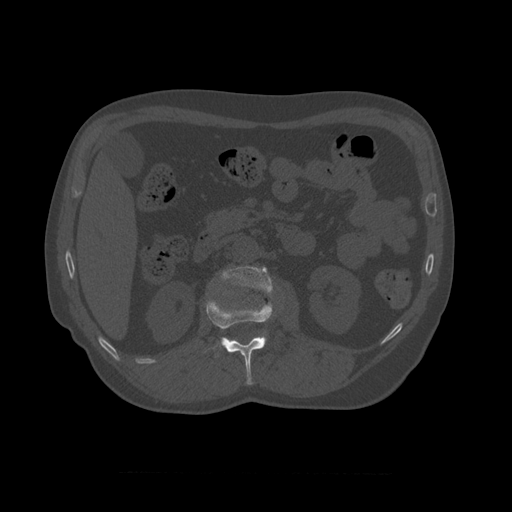
CT including the spine, one axial slice; position 349 of 450 along the scan axis; reconstruction kernel STANDARD; bone window (W 1800 / L 400 HU); 1.25 mm slice thickness; 512 × 512 image matrix, field of view 405 × 405 mm. Patient age 75 years. Case-level facts recorded for this patient, not image findings: primary cancer: prostate.
Outlined on this slice (semi-automatically segmented with operator editing):
- L1 vertebra: bounding box <205,289,274,385> (left, top, right, bottom; pixels)
- L2 vertebra: <218,266,274,348>